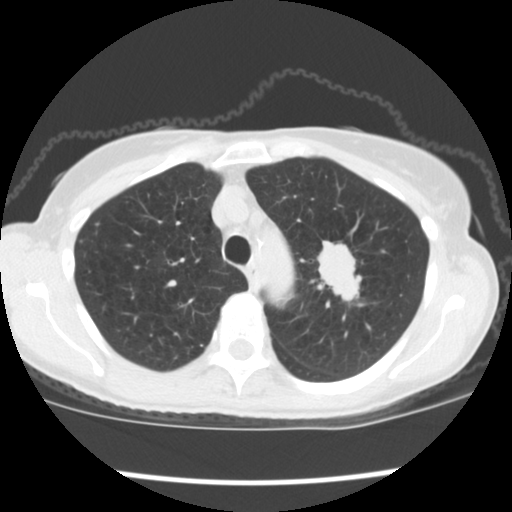
Chest CT (low-dose screening protocol), one axial image. First (baseline) screen. Lung window (W 1500 / L -600 HU). 2.5 mm slice thickness. Slice 37 of 176 in the series. 512 × 512 image matrix, field of view 318 × 318 mm. Female, age 67 years at enrolment.
Expert reader's lesion annotation, bounding box [x1, y1, x2, y2] px = [306, 234, 379, 310]. Screening reader's record for this exam (one nodule recorded; not confirmed to be the boxed lesion): non-calcified nodule or mass ≥4 mm, left upper lobe, 34 × 32 mm, spiculated (stellate) margins, soft tissue attenuation, pre-existing on the prior screen: no. Official screen result: positive, change unspecified: nodule(s) >= 4 mm or enlarging nodule(s), mass(es), or other non-specific abnormalities suspicious for lung cancer. Participant outcome: lung cancer diagnosed 17 days after this screen — small cell carcinoma, NOS, left upper lobe, stage IIIA (AJCC 6th edition), 40 mm at pathology.